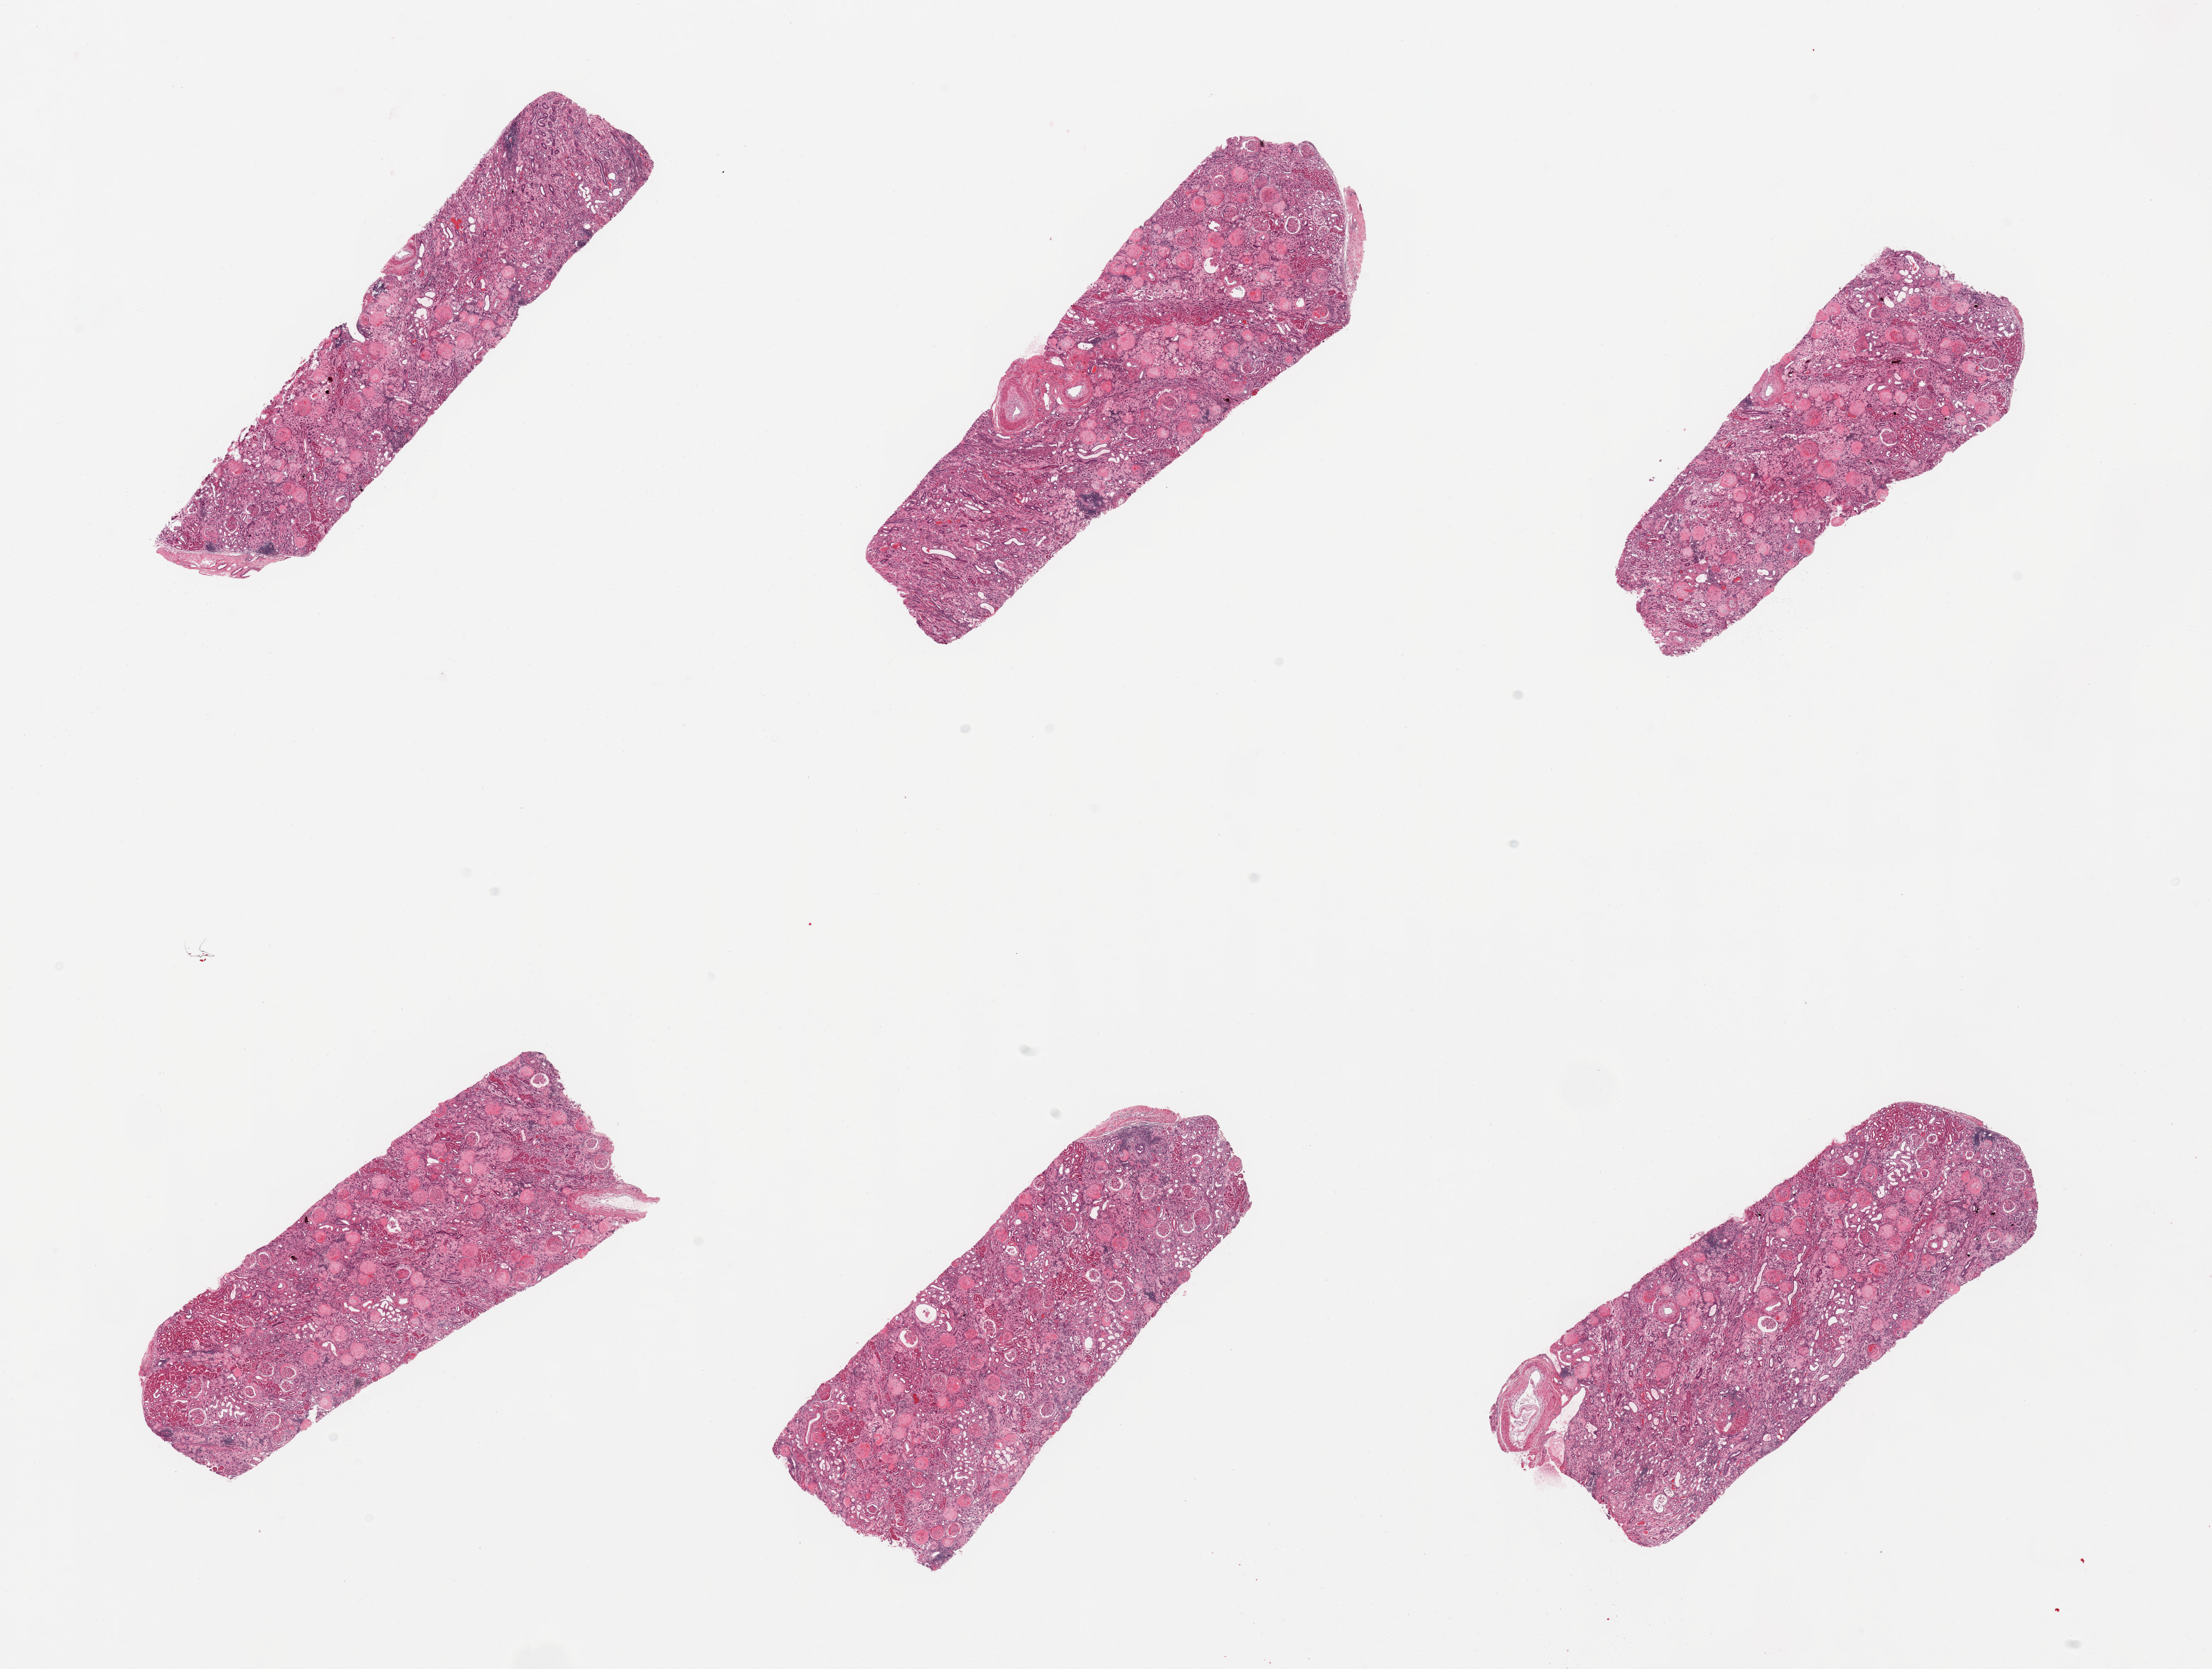
Hematoxylin and eosin (H&E) whole-slide image — shown as a low-resolution overview of the whole scanned area (about 24.6 x 18.6 mm); PAXgene-fixed paraffin-embedded (PFPE) section; sampled site (target tissue): renal cortex; tissue donor sample. Female donor.
* review note (as recorded): 6 pieces, glomeruli present--severe glomerulosclerosis, interstitial fibrosis and diabetic glomerulopathy